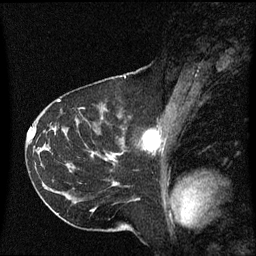
Breast MRI (dynamic contrast-enhanced), one sagittal slice. Position 35 of 60 along the scan axis. Dynamic contrast-enhanced series, image 2 of 3 at this slice position (ordered by acquisition). 1.5 T. TE 4.2 ms, TR 8.4 ms. 2 mm slice thickness. 256 × 256 image matrix, field of view 220 × 220 mm. Female patient, age 41 years. Case-level facts recorded for this patient, not image findings: setting: breast cancer imaged before/during neoadjuvant chemotherapy; receptor status: triple-negative.
Outlined on this slice (semi-automatically segmented with operator editing):
- analysis volume of interest (the breast-tissue region the enhancement analysis was run in; not a lesion): bounding box (x1, y1, x2, y2) in pixels: (116, 116, 159, 157)
- tumour enhancement mask (voxels above the 70 % enhancement threshold inside the analysis volume of interest): (145, 132, 159, 149)